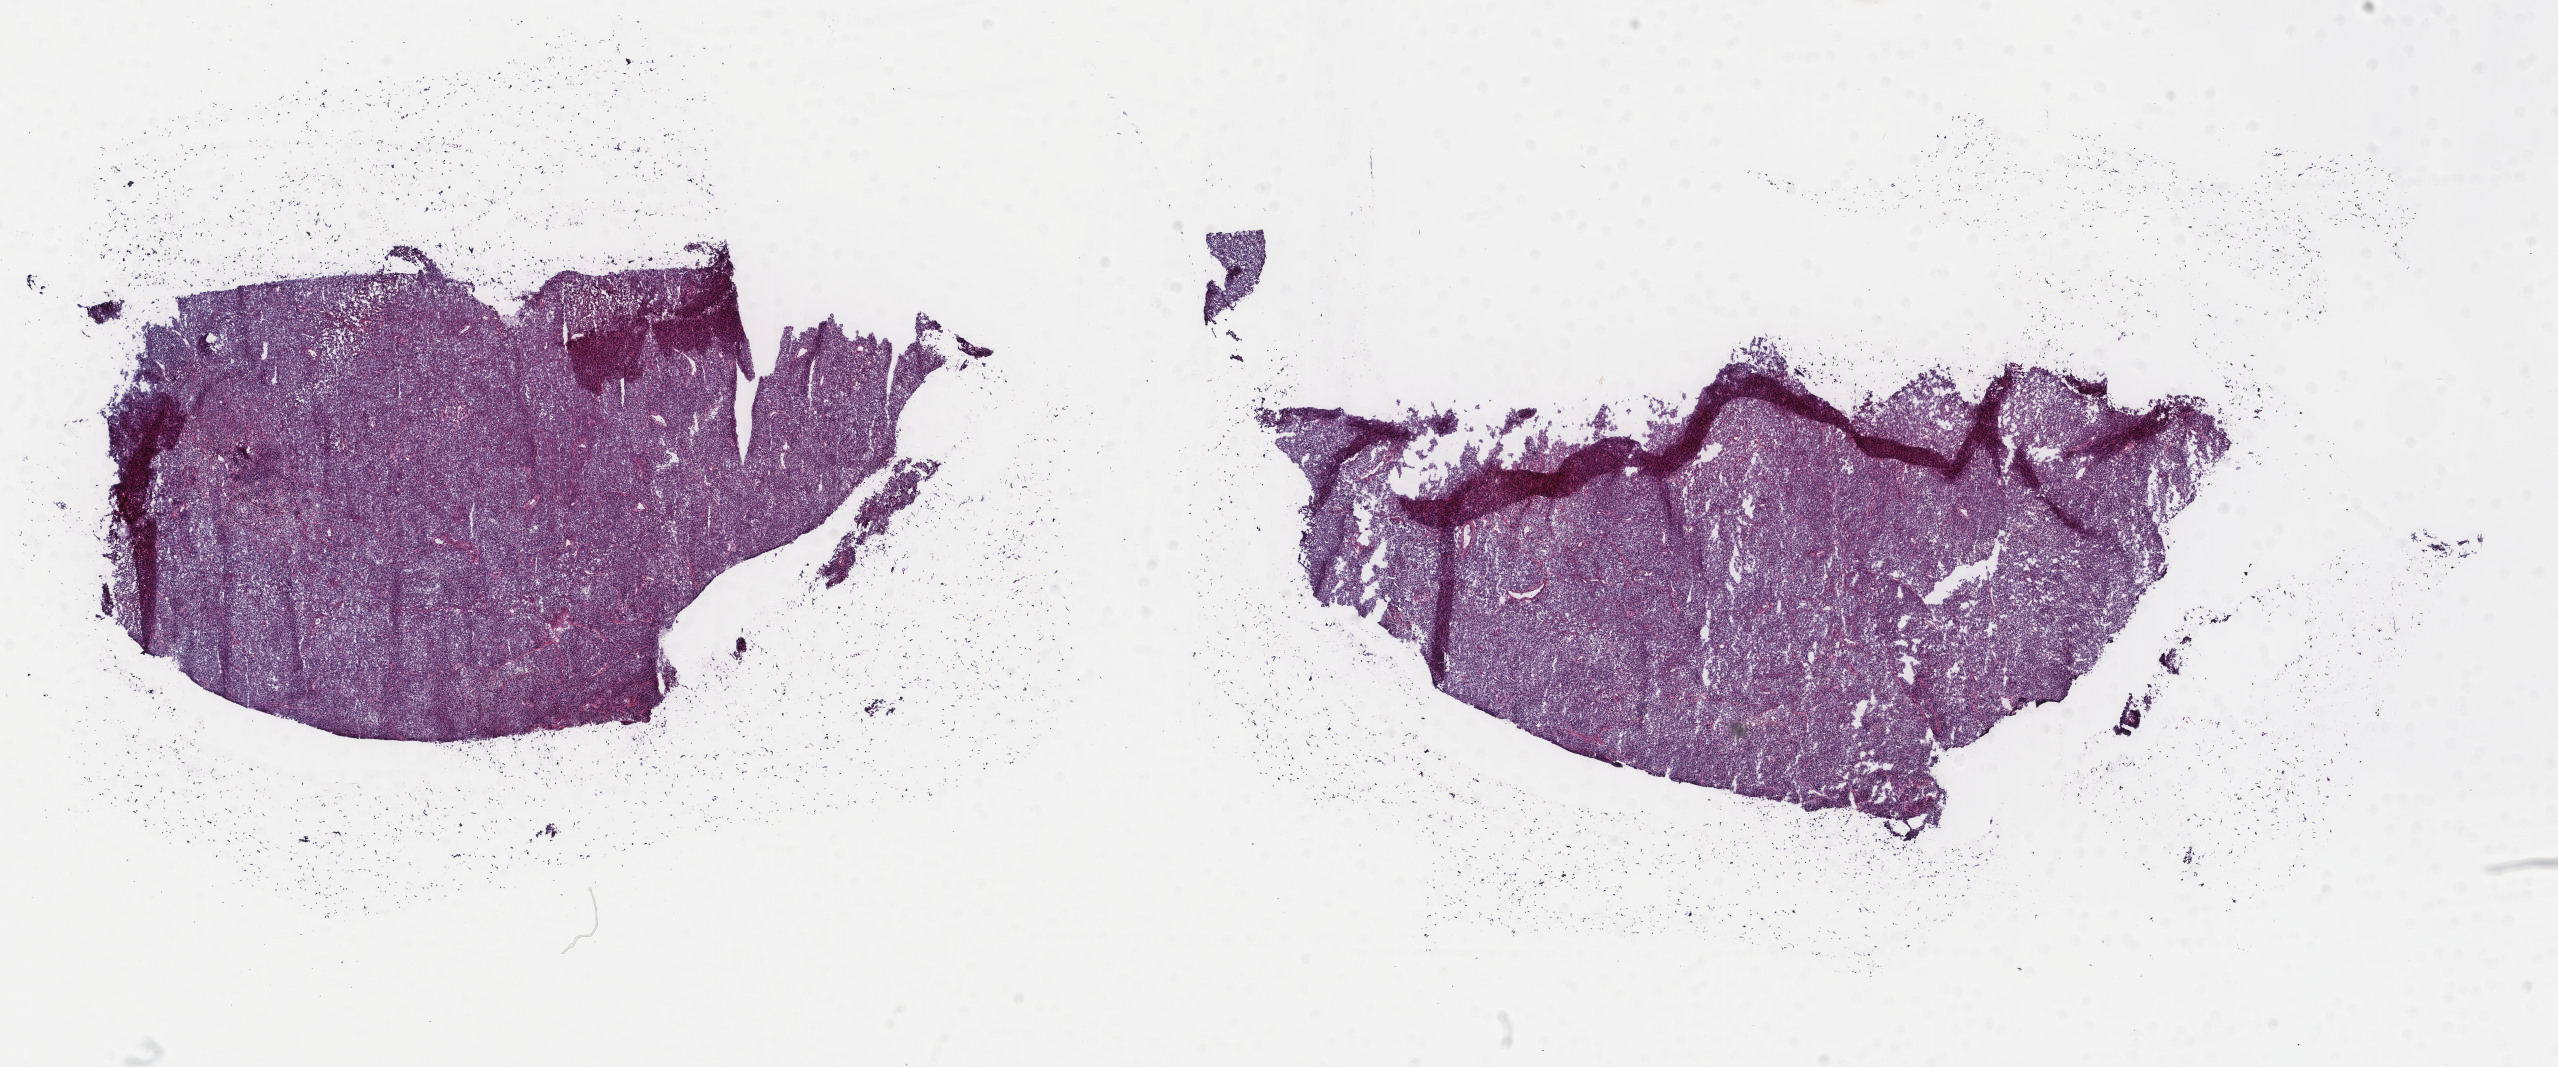
Digitized Hematoxylin and eosin (H&E) stained tissue section (whole slide), low-resolution overview of the scanned area, about 20.3 x 8.5 mm (acquisition: 40x scan). Frozen section from the top of the tissue portion. Metastatic tumour sample, sampled site not recorded. Male, age 72 years at initial diagnosis. Pathologist review of this section (percent, as recorded): tumour cells 90%, tumour nuclei 90%.
This section: metastatic tumour tissue. Patient diagnosis: Malignant melanoma, NOS.